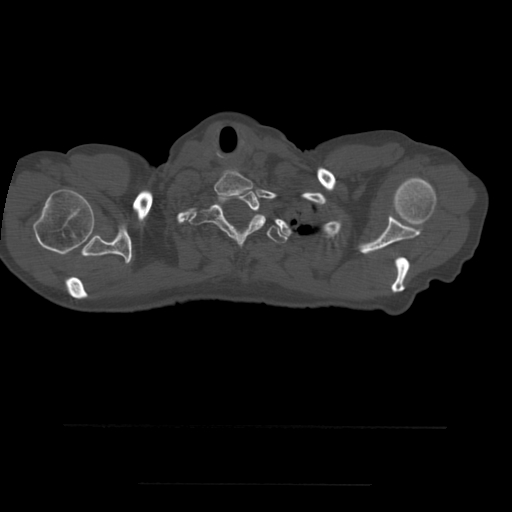
CT including the spine, one axial slice. Position 445 of 544 along the scan axis. Bone window (W 1800 / L 400 HU). 1.25 mm slice thickness. 512 × 512 image matrix, field of view 350 × 350 mm. Patient age 58 years. From the clinical record (not read from this slice): primary cancer: lung.
Outlined on this slice (semi-automatically segmented with operator editing):
- T1 vertebra: bounding box <188,190,266,246> (left, top, right, bottom; pixels)
- T2 vertebra: <255,215,288,243>